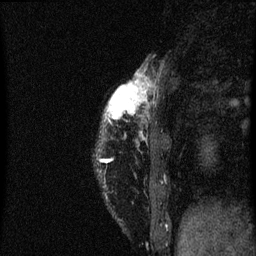
Breast MRI (dynamic contrast-enhanced), one sagittal slice. Dynamic contrast-enhanced series, image 2 of 3 at this slice position (ordered by acquisition). 1.5 T. TE 4.2 ms, TR 8 ms. 2 mm slice thickness. 256 × 256 image matrix, field of view 180 × 180 mm. Female patient, age 38 years.
Outlined on this slice (semi-automatically segmented with operator editing):
- analysis volume of interest (the breast-tissue region the enhancement analysis was run in; not a lesion): bounding box [x1, y1, x2, y2] px = [104, 76, 149, 123]
- tumour enhancement mask (voxels above the 70 % enhancement threshold inside the analysis volume of interest): [108, 80, 147, 119]